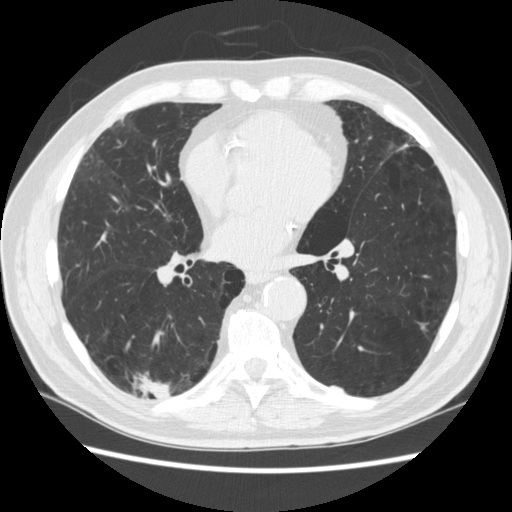
Low-dose screening chest CT, one axial slice. Position 122 of 266 along the scan axis. Reconstruction kernel STANDARD. 120 kVp. Lung window (W 1500 / L -600 HU). 1.25 mm slice thickness. 512 × 512 image matrix, field of view 360 × 360 mm.
Structures marked on this image (expert manual segmentation):
- lesion 1 (tumor, upper lobe of right lung): box from (x=141, y=378) to (x=170, y=399) px